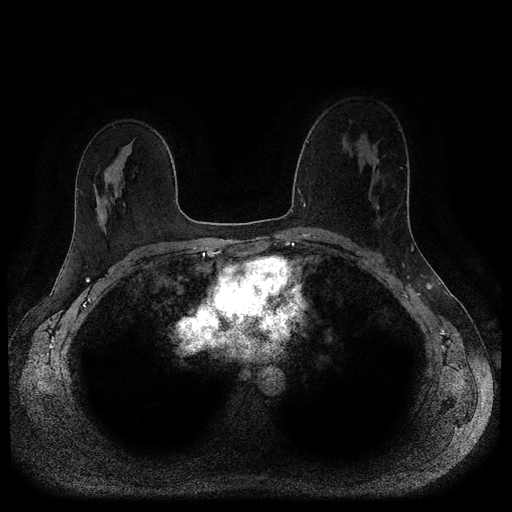
Breast MRI (dynamic contrast-enhanced, multi-phase), one axial slice. Slice 63 of 116 in the series (ordered by position). Dynamic contrast-enhanced series, time point 2 of 5 at this slice position (early post-contrast). 1.5 T. TE 2.6 ms, TR 5.3 ms. 2 mm slice thickness. 512 × 512 image matrix, field of view 350 × 350 mm. Patient: female, 45 years.
Structures marked on this image (semi-automatic segmentation, software-assisted and operator-edited):
- breast lesion (labelled 'tumour' in the annotation; benign lesions carry a separate 'benign' label): bounding box <375,159,380,210> (left, top, right, bottom; pixels)